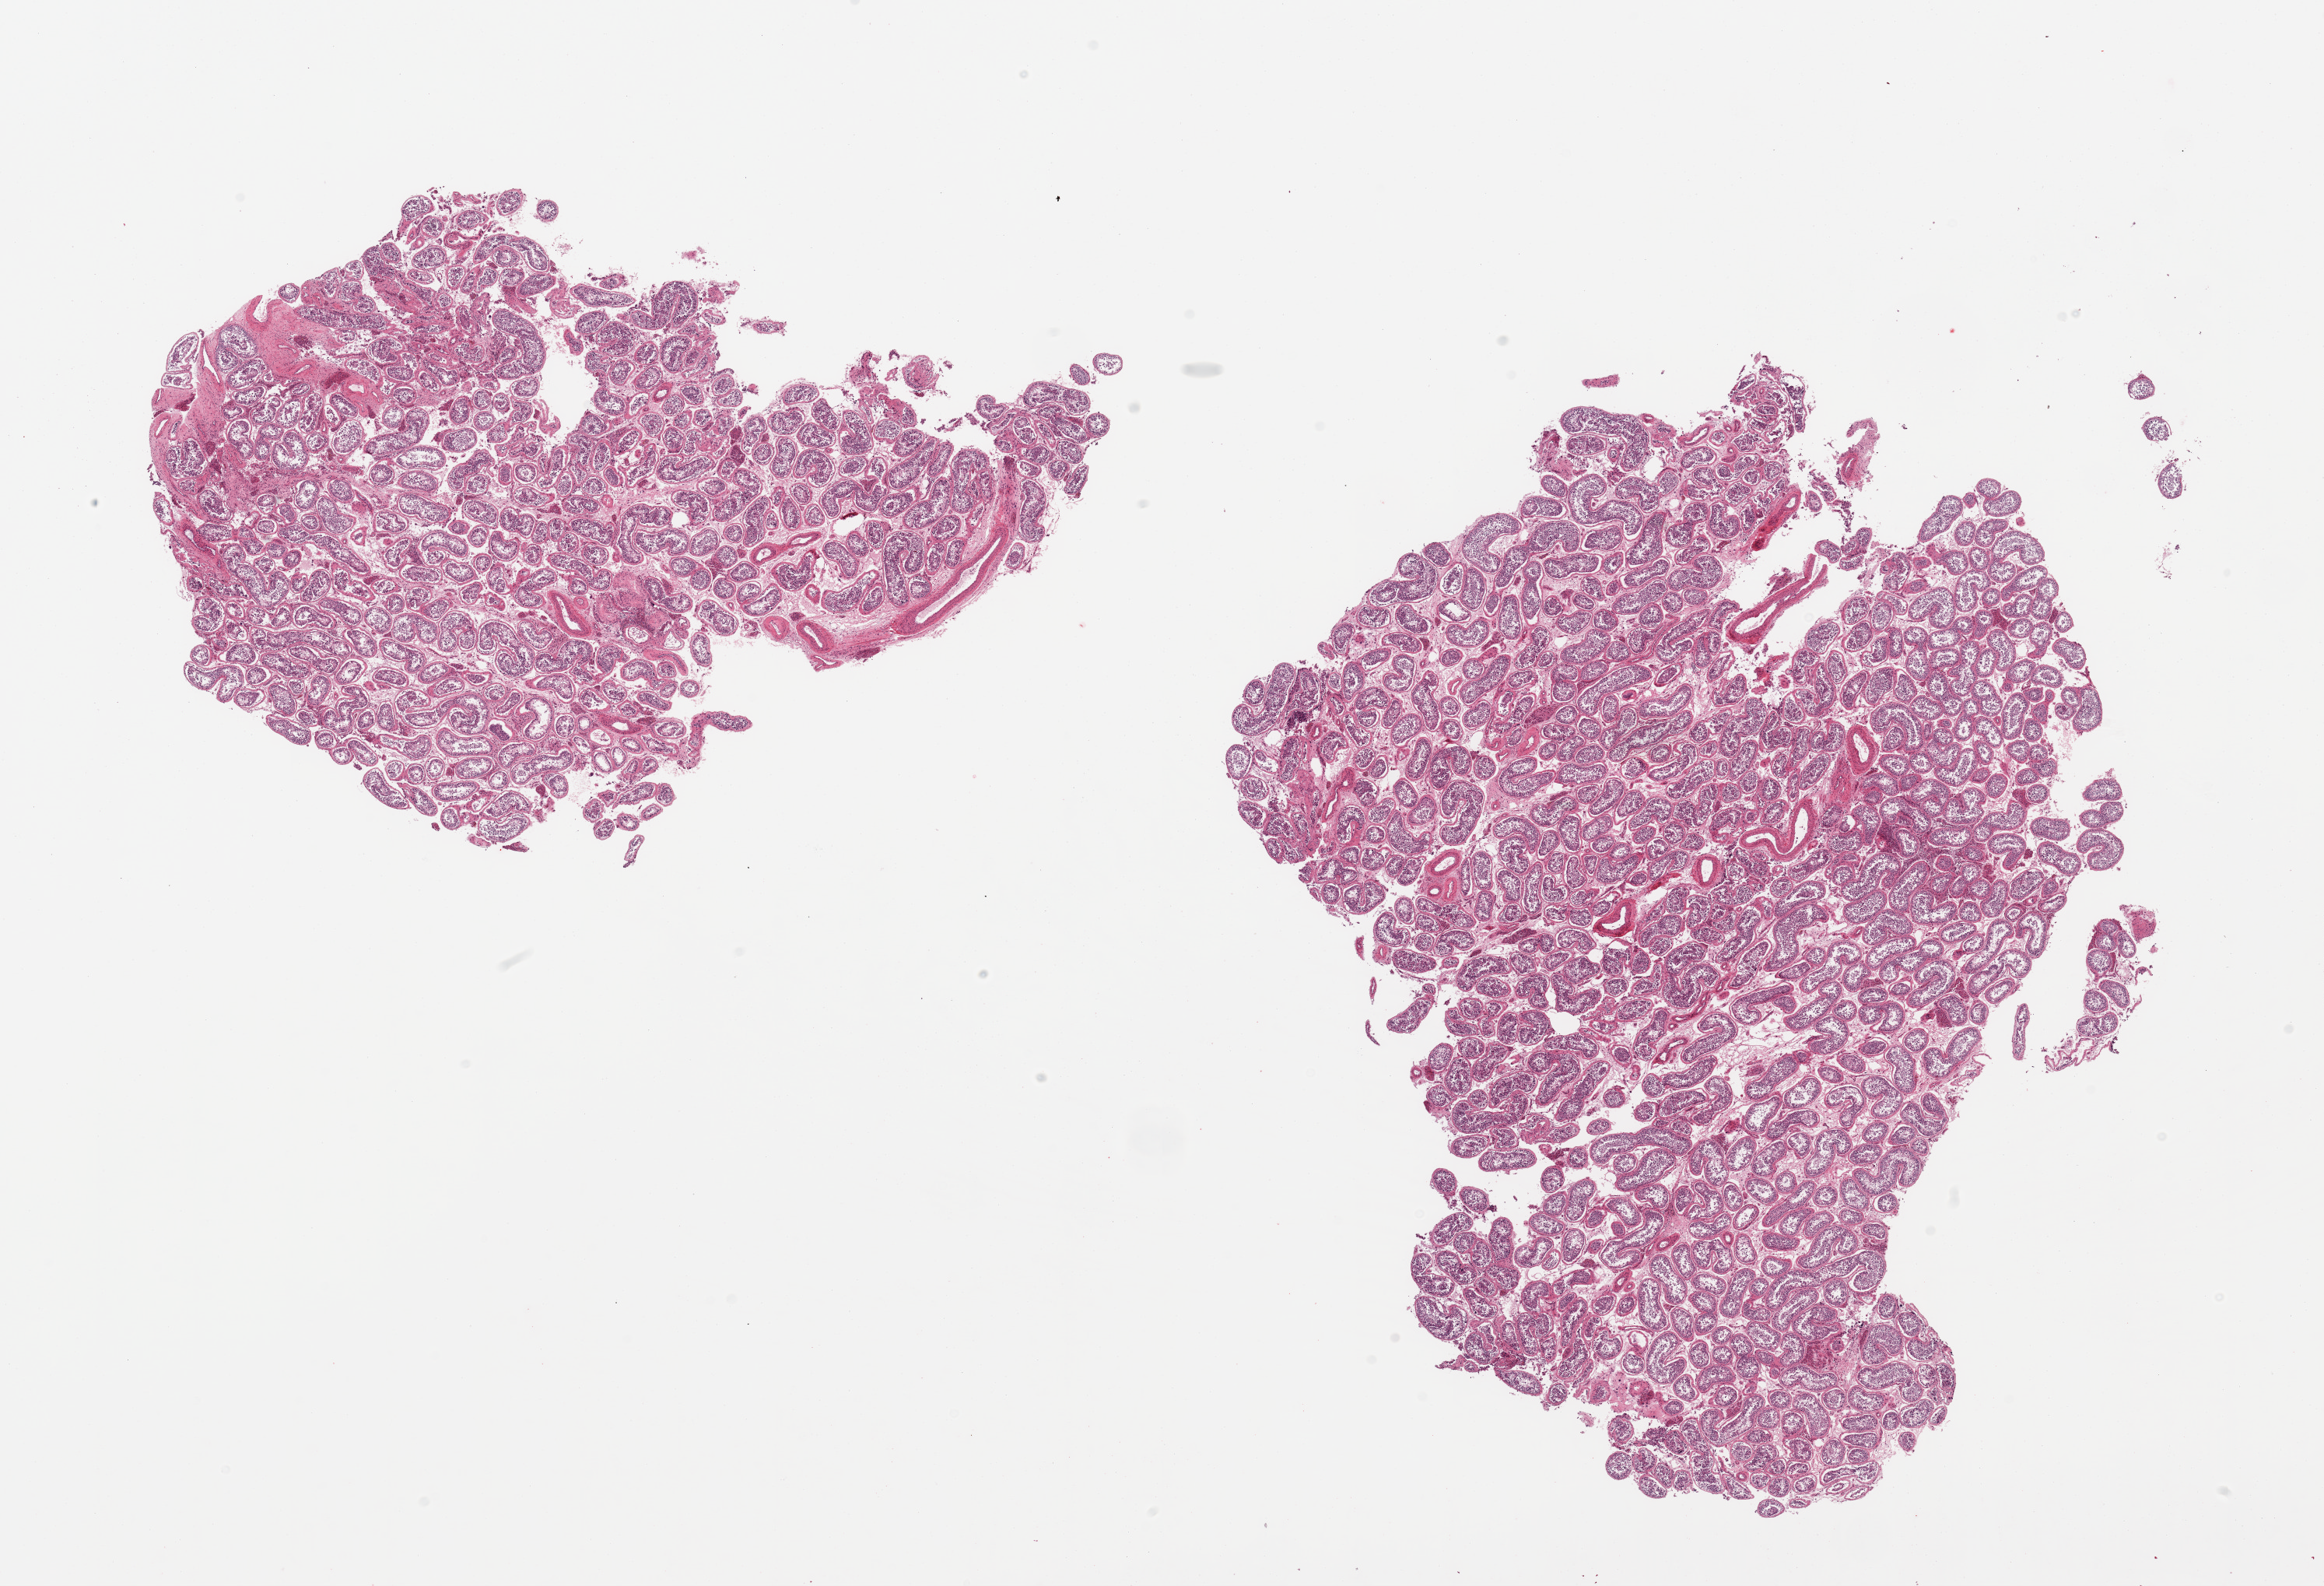
Whole-slide image, H&E stain, whole scanned area (about 23.6 x 16.1 mm, acquisition: 20x scan) shown as a low-resolution overview, PAXgene-fixed, paraffin-embedded tissue, target tissue: testis, tissue donor sample. Male donor.
Pathologist's review note for this sample: 2 pieces, spermatogenesis is present.